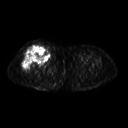
FDG PET of an extremity soft-tissue mass (from a PET/CT study), one axial slice. Slice 259 of 311 in the series (ordered by position). 128 × 128 image matrix, field of view 500 × 500 mm. Female patient, age 57 years. From the clinical record (not read from this slice): histological type: pleiomorphic undifferentiated sarcoma; grade: high; site of the primary tumour: right quadricep.
Annotated regions visible in this slice (expert contour drawn on MRI and transferred to this co-registered scan by the dataset authors):
- tumour plus oedema (research contour): bounding box (x1, y1, x2, y2) in pixels: (22, 45, 50, 71)
- tumour (research contour): (22, 45, 50, 71)